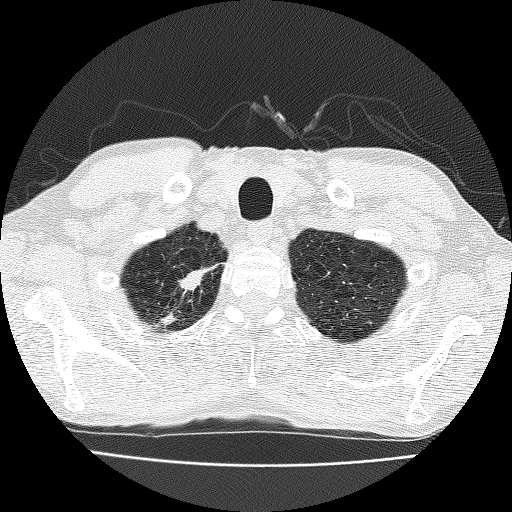
Low-dose screening chest CT, one axial slice; slice 160 of 185 in the series (ordered by position); lung window (W 1500 / L -600 HU); 2 mm slice thickness; 512 × 512 image matrix.
Outlined on this slice (expert manual segmentation):
- lesion 1 (nodule, upper lobe of right lung): bounding box (x1, y1, x2, y2) in pixels: (178, 268, 207, 291)
- lesion 2 (nodule, upper lobe of right lung): (163, 314, 173, 324)